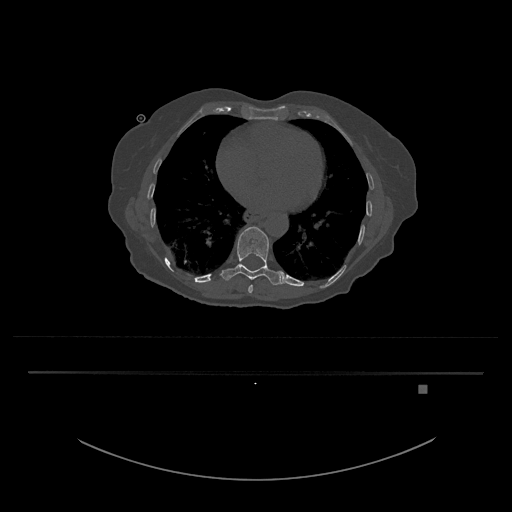
CT including the spine, one axial slice. Slice 718 of 797 in the series (ordered by position). Reconstruction kernel Br40s/3. 120 kVp. Bone window (W 1800 / L 400 HU). 0.5 mm slice thickness. 512 × 512 image matrix, field of view 500 × 500 mm. Female patient, age 57 years. From the clinical record (not read from this slice): primary cancer: cervical.
Outlined on this slice (semi-automatically segmented with operator editing):
- T10 vertebra: bounding box [x1, y1, x2, y2] px = [221, 226, 284, 285]
- T9 vertebra: [248, 285, 253, 294]